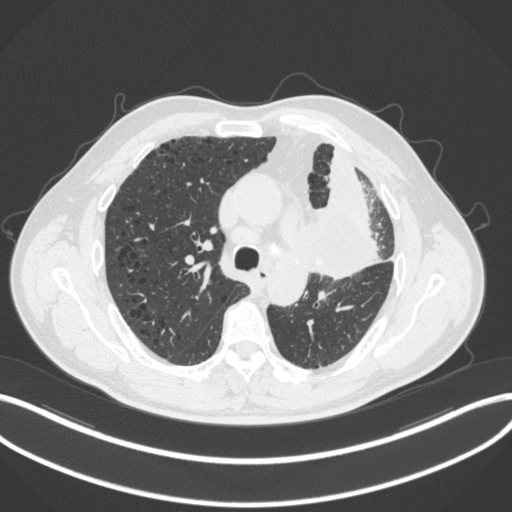
Chest CT, one axial slice. Slice 195 of 286 in the series (ordered by position). Reconstruction kernel B31f. 120 kVp. Lung window (W 1500 / L -600 HU). 1 mm slice thickness. 512 × 512 image matrix, field of view 400 × 400 mm. Male patient, age 68 years. From the clinical record (not read from this slice): clinical TNM (as recorded): T3 N3 M1.
Outlined on this slice (bounding box drawn by a radiologist):
- lung tumour (recorded histology: adenocarcinoma): bounding box (x1, y1, x2, y2) in pixels: (294, 199, 387, 283)